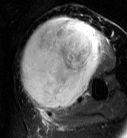
MRI of an extremity soft-tissue mass, one axial slice; position 42 of 87 along the scan axis; T2-weighted fat-saturated; MR volume resampled by the dataset authors to the PET/CT grid (not the native acquisition matrix); 3.27 mm slice thickness; 127 × 138 image matrix, field of view 124 × 135 mm. Female patient. Case-level facts recorded for this patient, not image findings: histological type: pleiomorphic leiomyosarcoma; grade: high; site of the primary tumour: left biceps.
Structures marked on this image (expert contour drawn on MRI and transferred to this co-registered scan by the dataset authors):
- gross tumour volume including surrounding oedema: box from (x=20, y=18) to (x=107, y=113) px
- gross tumour volume (mass): (x=20, y=18)–(x=101, y=111)